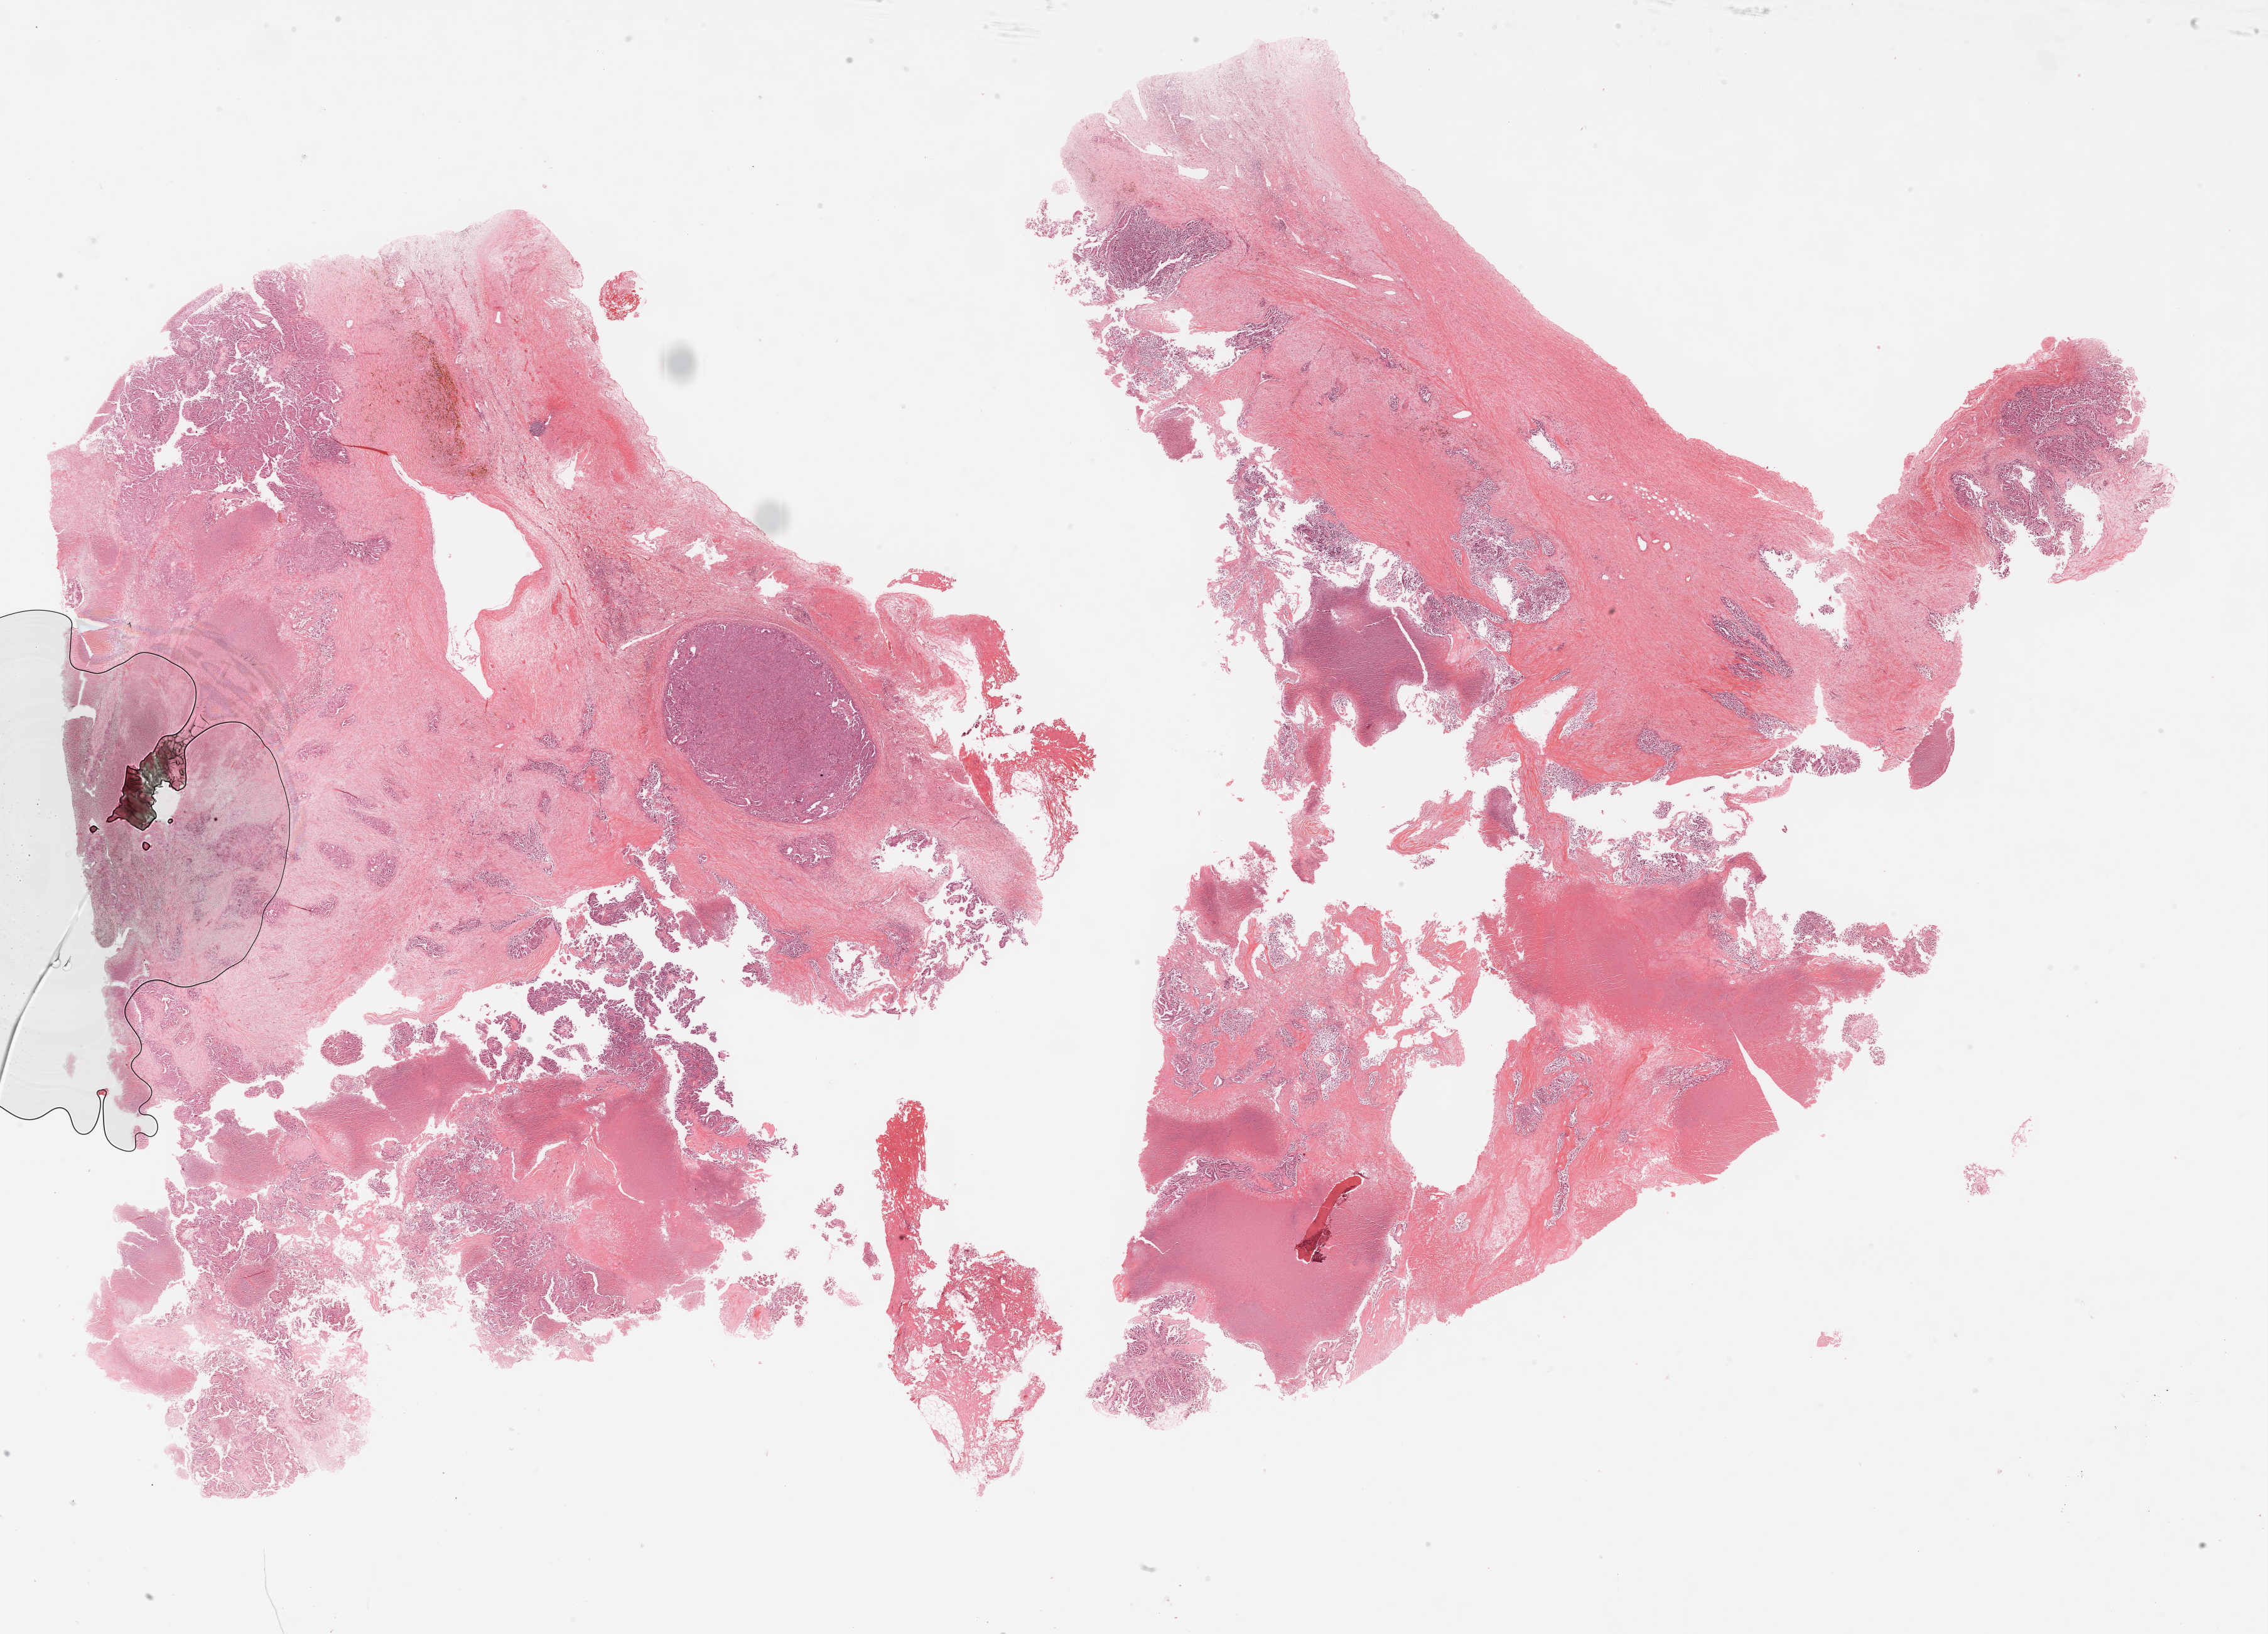
H&E-stained whole-slide image, a low-resolution overview of the entire scanned area, about 29.2 x 21.0 mm; formalin-fixed paraffin-embedded (FFPE) diagnostic section; ovary, primary tumour sample. Female, age 73 years at initial diagnosis. Histologic grade: G3 (poorly differentiated).
FIGO stage: IIIC. Pathologic diagnosis: Serous cystadenocarcinoma, NOS.